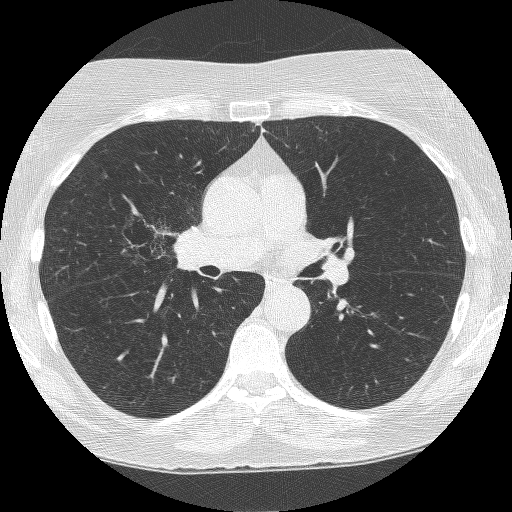
Low-dose screening chest CT, axial slice. Second annual screen. Lung window (W 1500 / L -600 HU). 1.25 mm slice thickness. 120 kVp. Female, age 64 years at enrolment. Former smoker at enrolment.
Expert reader's lesion annotation, box from (x=117, y=206) to (x=201, y=287) px. The screening reader recorded 4 non-calcified nodules or masses ≥4 mm on this exam; which of them this box marks is not recorded. Official screen result: positive, other. Later outcome: lung cancer diagnosed 381 days after this screen — adenocarcinoma, NOS, right upper lobe, right middle lobe, right hilum, stage IV (AJCC 6th edition), 85 mm at pathology.